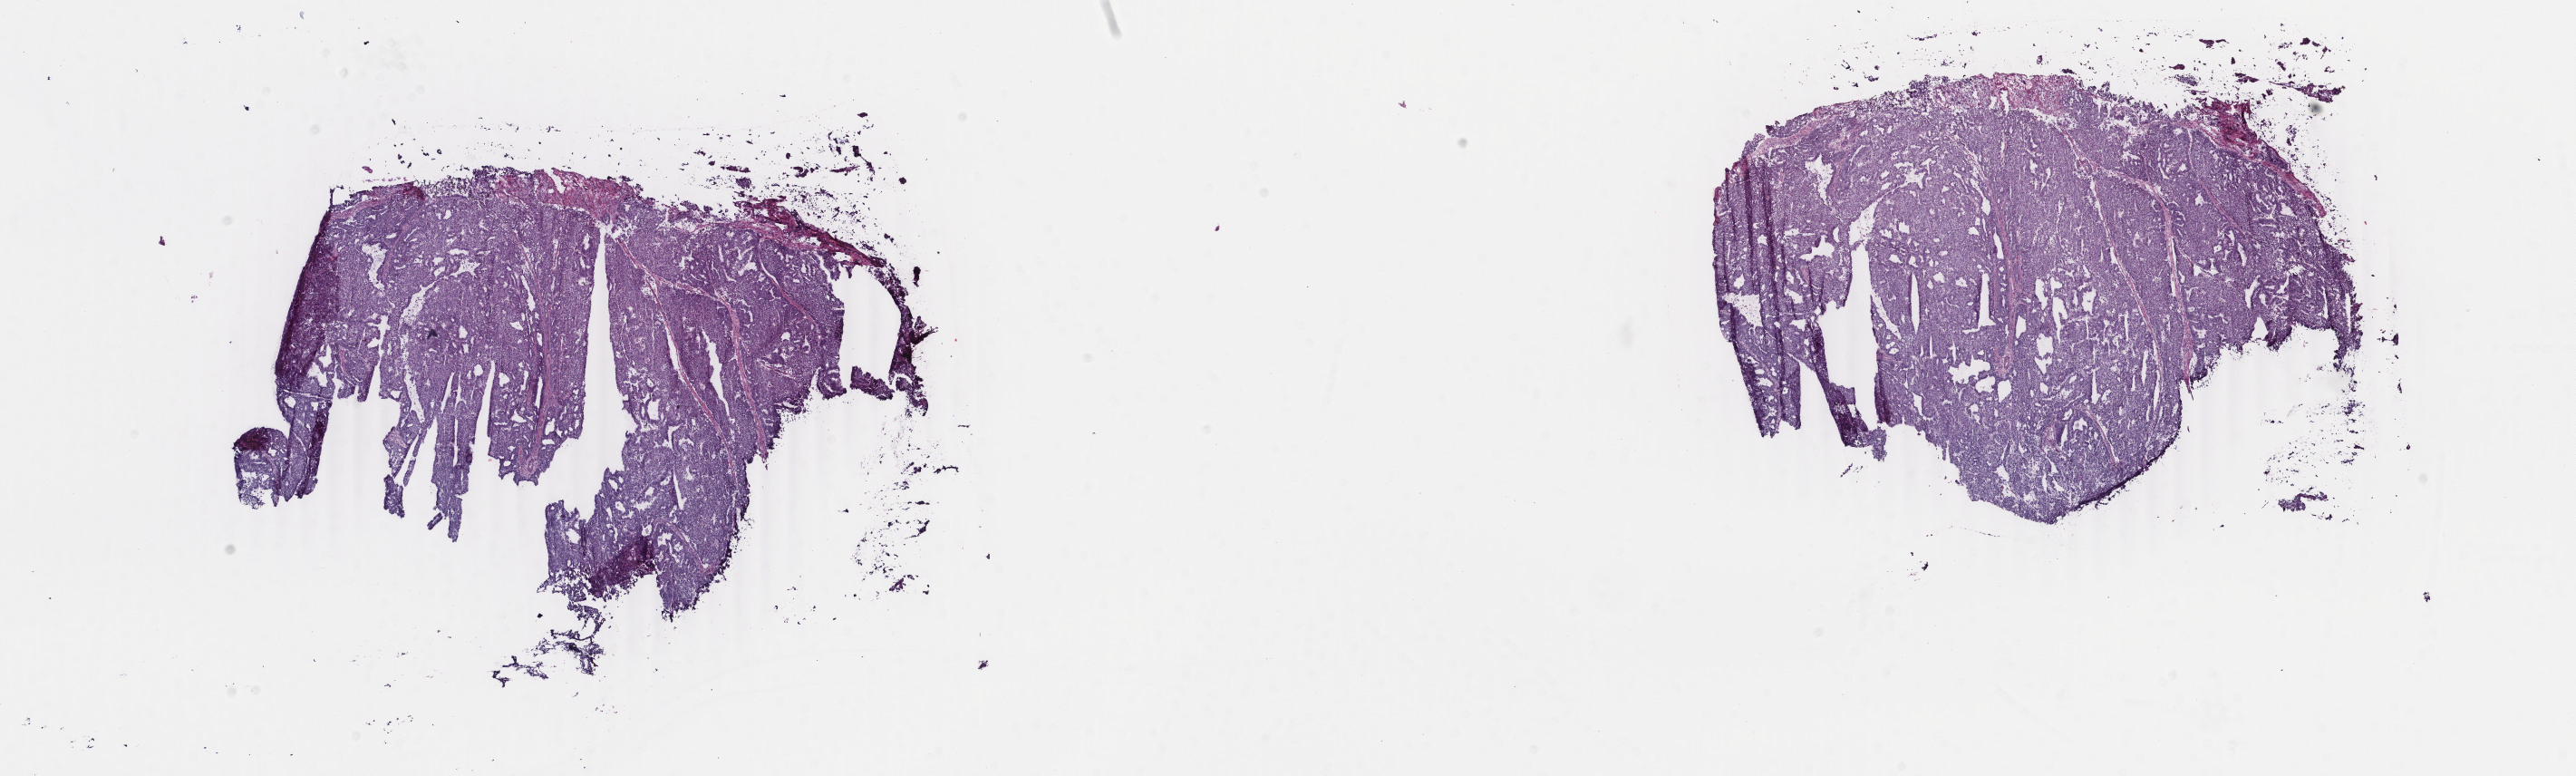
Digitized Hematoxylin and eosin (H&E) stained tissue section (whole slide), a low-resolution overview of the entire scanned area, about 22.6 x 6.8 mm, frozen section from the bottom of the tissue portion, uterus, primary tumour sample. Female, age 47 years at initial diagnosis. Histologic grade: G2 (moderately differentiated). Slide review estimates, as recorded: tumour cells 80%, tumour nuclei 90%, normal cells 10%, stromal cells 0%, necrosis 10%. Infiltration values recorded for this section: lymphocyte infiltration 10%, monocyte infiltration 0%, neutrophil infiltration 0%.
FIGO stage: IB. Diagnosis: Endometrioid adenocarcinoma, NOS (endometrium).